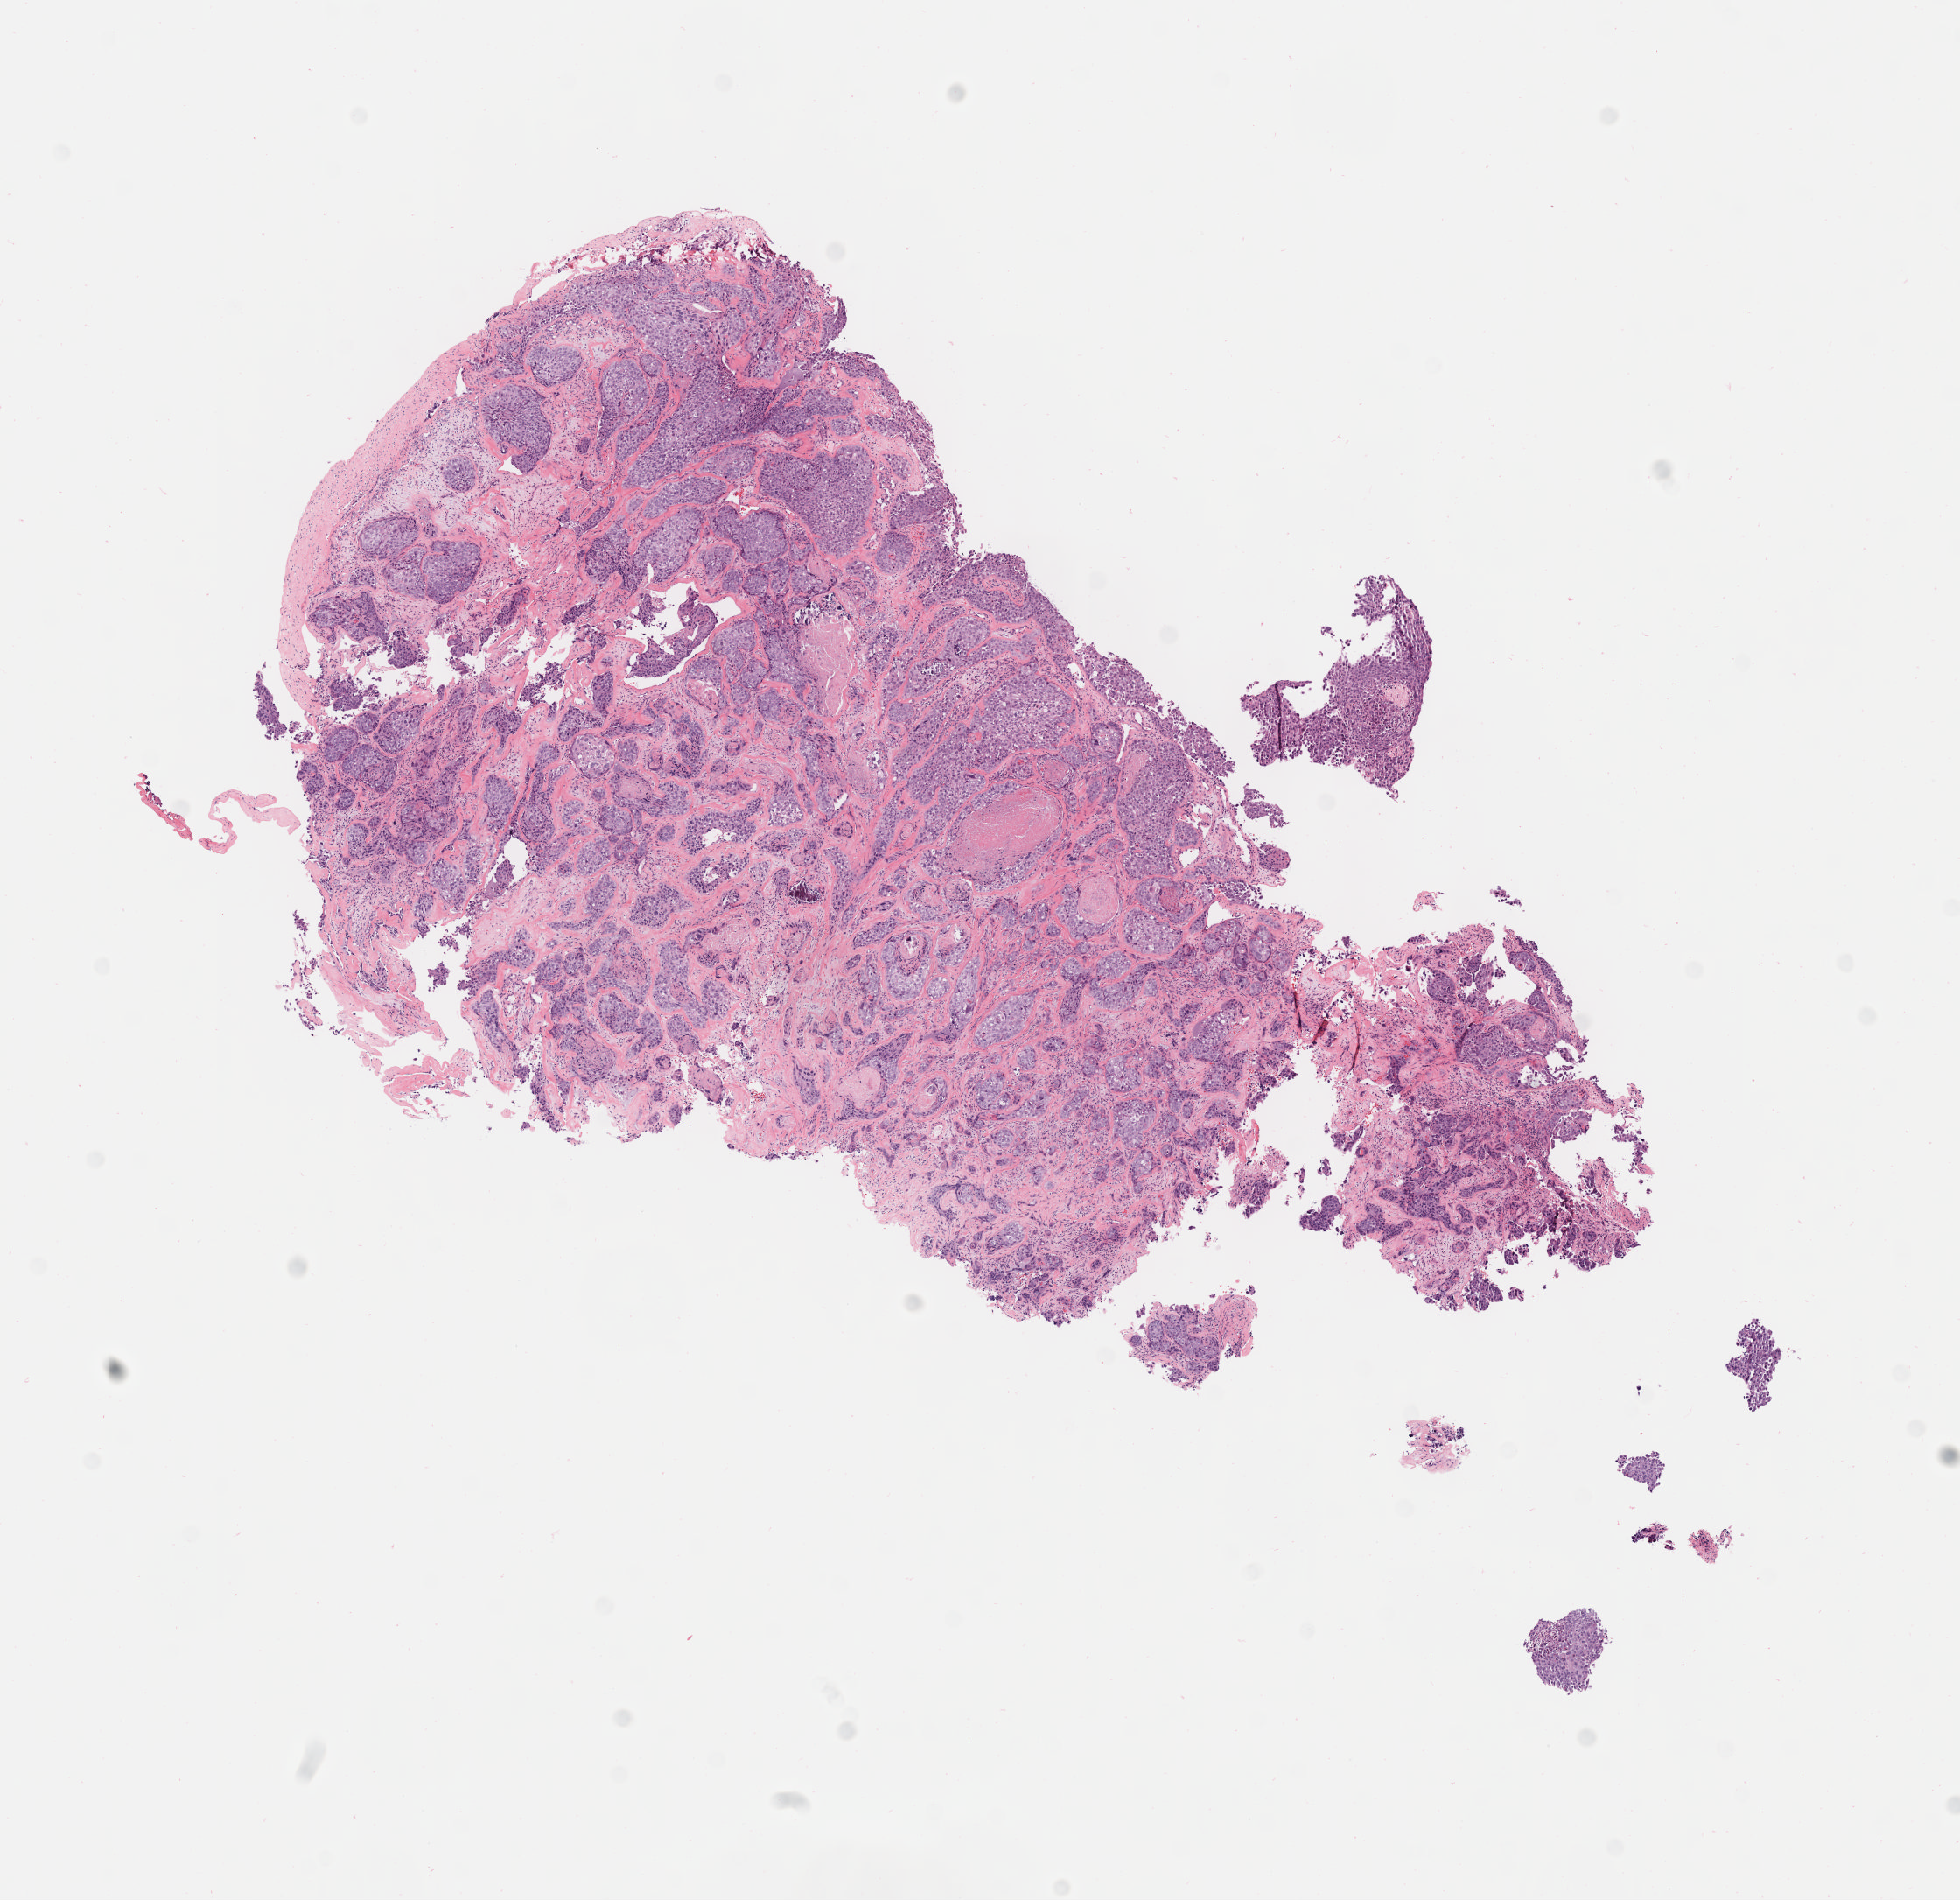
Hematoxylin and eosin (H&E) whole-slide image — shown as a low-resolution overview of the whole scanned area (about 9.1 x 8.8 mm); specimen: tumor tissue; anatomic site: cervix. Patient: female, 67 years old.
Histologic diagnosis: Squamous cell carcinoma, keratinizing, NOS.